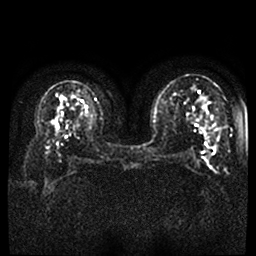
Breast MRI, one axial slice. Position 19 of 45 along the scan axis. Diffusion-weighted series; image 2 of 4 stored at this slice position (different b-values; order by instance number). 1.5 T. 4 mm slice thickness. 256 × 256 image matrix, field of view 340 × 340 mm. Female patient.
Annotated regions visible in this slice (expert manual segmentation):
- tumour on diffusion-weighted imaging: bounding box (x1, y1, x2, y2) in pixels: (205, 147, 215, 170)